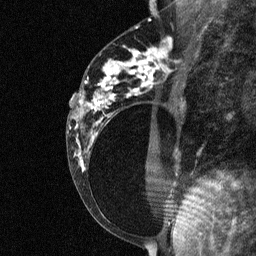
Breast MRI (dynamic contrast-enhanced), one sagittal slice. Slice 31 of 64 in the series (ordered by position). Dynamic contrast-enhanced study with each time point stored as its own series, time point 2 of 3 at this slice position (early post-contrast, ordered by acquisition time). 1.5 T. TE 4.8 ms, TR 27 ms. 256 × 256 image matrix, field of view 180 × 180 mm. Patient: female, 34 years. From the clinical record (not read from this slice): setting: breast cancer imaged before/during neoadjuvant chemotherapy; receptor status: HR-positive, HER2-negative.
Annotated regions visible in this slice (semi-automatic segmentation, software-assisted and operator-edited):
- analysis volume of interest (the breast-tissue region the enhancement analysis was run in; not a lesion): bounding box <78,44,181,191> (left, top, right, bottom; pixels)
- tumour enhancement mask (voxels above the 90 % enhancement threshold inside the analysis volume of interest): <82,49,163,166>